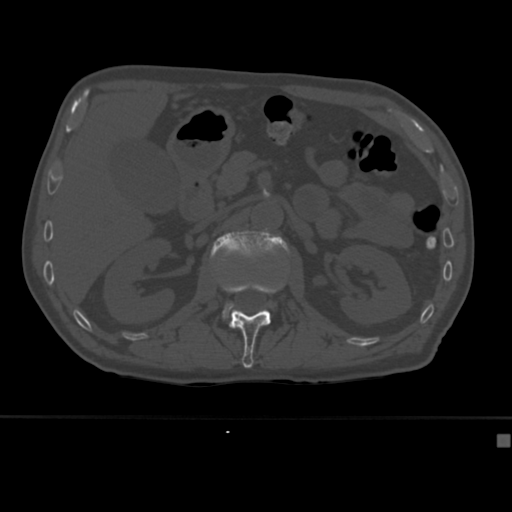
CT including the spine, one axial slice. Position 163 of 430 along the scan axis. Bone window (W 1800 / L 400 HU). 512 × 512 image matrix, field of view 337 × 337 mm. Male patient, age 64 years. Case-level facts recorded for this patient, not image findings: primary cancer: uterus; vertebrae with lytic lesions (as recorded): T1, T4, T5, T7, L5.
Outlined on this slice (semi-automatically segmented with operator editing):
- L1 vertebra: bounding box (x1, y1, x2, y2) in pixels: (210, 255, 284, 368)
- L2 vertebra: (211, 231, 290, 319)